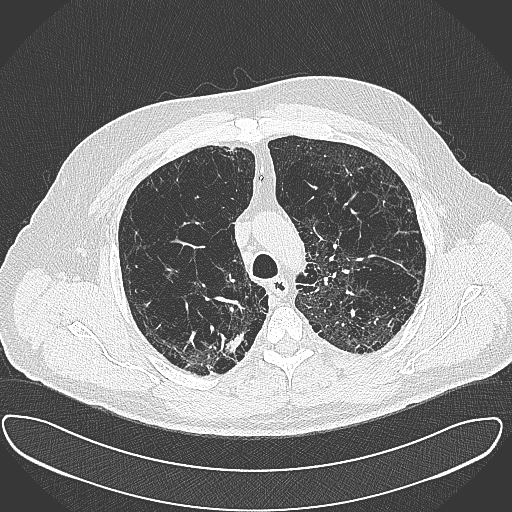
Low-dose screening chest CT, axial slice, baseline screening round, lung window (W 1500 / L -600 HU), 1 mm slice thickness, lung (sharp) reconstruction kernel (B80f), slice 94 of 385 in the series, 512 × 512 image matrix, field of view 408 × 408 mm. Male, age 60 years at enrolment. Current smoker at enrolment.
Lesion marked by an expert reader, bounding box [x1, y1, x2, y2] px = [192, 327, 250, 379]. Screening reader's record for this exam (one nodule recorded; not confirmed to be the boxed lesion): non-calcified nodule or mass ≥4 mm, right upper lobe, 15 × 25 mm, spiculated (stellate) margins, soft tissue attenuation. Official screen result: positive, change unspecified: nodule(s) >= 4 mm or enlarging nodule(s), mass(es), or other non-specific abnormalities suspicious for lung cancer. Lung cancer was diagnosed 32 days after this screen: carcinoma, NOS, right upper lobe, moderately differentiated (G2), stage IB (AJCC 6th edition), 35 mm at pathology.